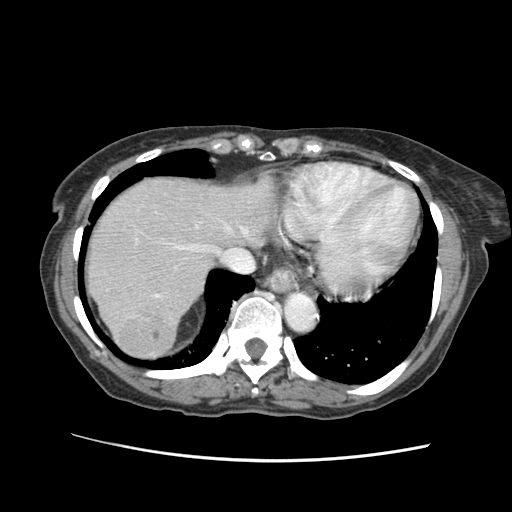
Contrast-enhanced abdominal CT (liver protocol), one axial slice. Slice 51 of 63 in the series (ordered by position). Reconstruction kernel STANDARD. 120 kVp. Soft-tissue window (W 400 / L 40 HU). 2.5 mm slice thickness. 512 × 512 image matrix, field of view 340 × 340 mm. Case-level facts recorded for this patient, not image findings: diagnosis: hepatocellular carcinoma (patient treated with transarterial chemoembolisation; whether this scan precedes or follows treatment is not stated here); TNM stage (as recorded): Stage-I; Child-Pugh class: B; tumour differentiation: well differentiated.
Annotated regions visible in this slice (semi-automatic segmentation, software-assisted and operator-edited):
- liver parenchyma outside the tumour (the mass and vessels are separate outlines, so this box may not span the whole liver): bounding box <88,178,274,354> (left, top, right, bottom; pixels)
- mass: <111,299,172,353>
- liver vessels: <154,229,245,349>